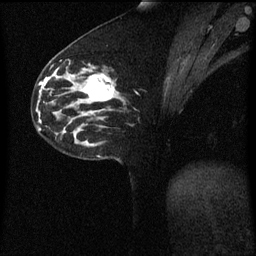
Breast MRI (dynamic contrast-enhanced), one sagittal slice. Position 27 of 60 along the scan axis. Dynamic contrast-enhanced series, image 2 of 3 at this slice position (ordered by acquisition). 1.5 T. TE 4.2 ms, TR 8.4 ms. 2 mm slice thickness. 256 × 256 image matrix, field of view 200 × 200 mm. Female patient, age 33 years. Case-level facts recorded for this patient, not image findings: setting: breast cancer imaged before/during neoadjuvant chemotherapy; receptor status: triple-negative.
Structures marked on this image (semi-automatic segmentation, software-assisted and operator-edited):
- analysis volume of interest (the breast-tissue region the enhancement analysis was run in; not a lesion): bounding box [x1, y1, x2, y2] px = [76, 64, 123, 113]
- tumour enhancement mask (voxels above the 70 % enhancement threshold inside the analysis volume of interest): [82, 74, 114, 101]